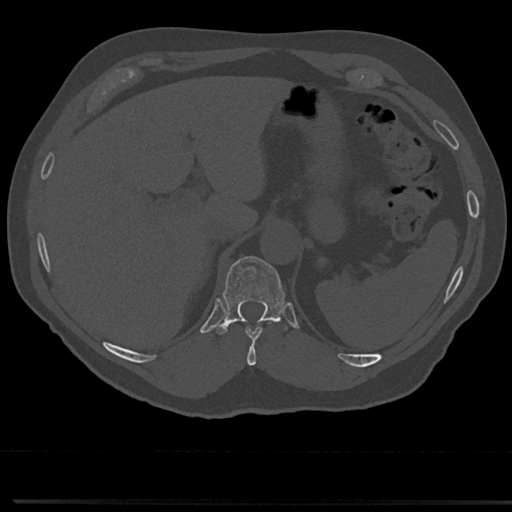
CT including the spine, one axial slice. Slice 222 of 817 in the series (ordered by position). Reconstruction kernel Br40s/3. 120 kVp. Bone window (W 1800 / L 400 HU). 0.5 mm slice thickness. 512 × 512 image matrix. Patient: male, 61 years. Case-level facts recorded for this patient, not image findings: primary cancer: prostate.
Structures marked on this image (semi-automatic segmentation, software-assisted and operator-edited):
- T10 vertebra: bounding box <244,320,277,366> (left, top, right, bottom; pixels)
- T11 vertebra: <223,256,284,322>